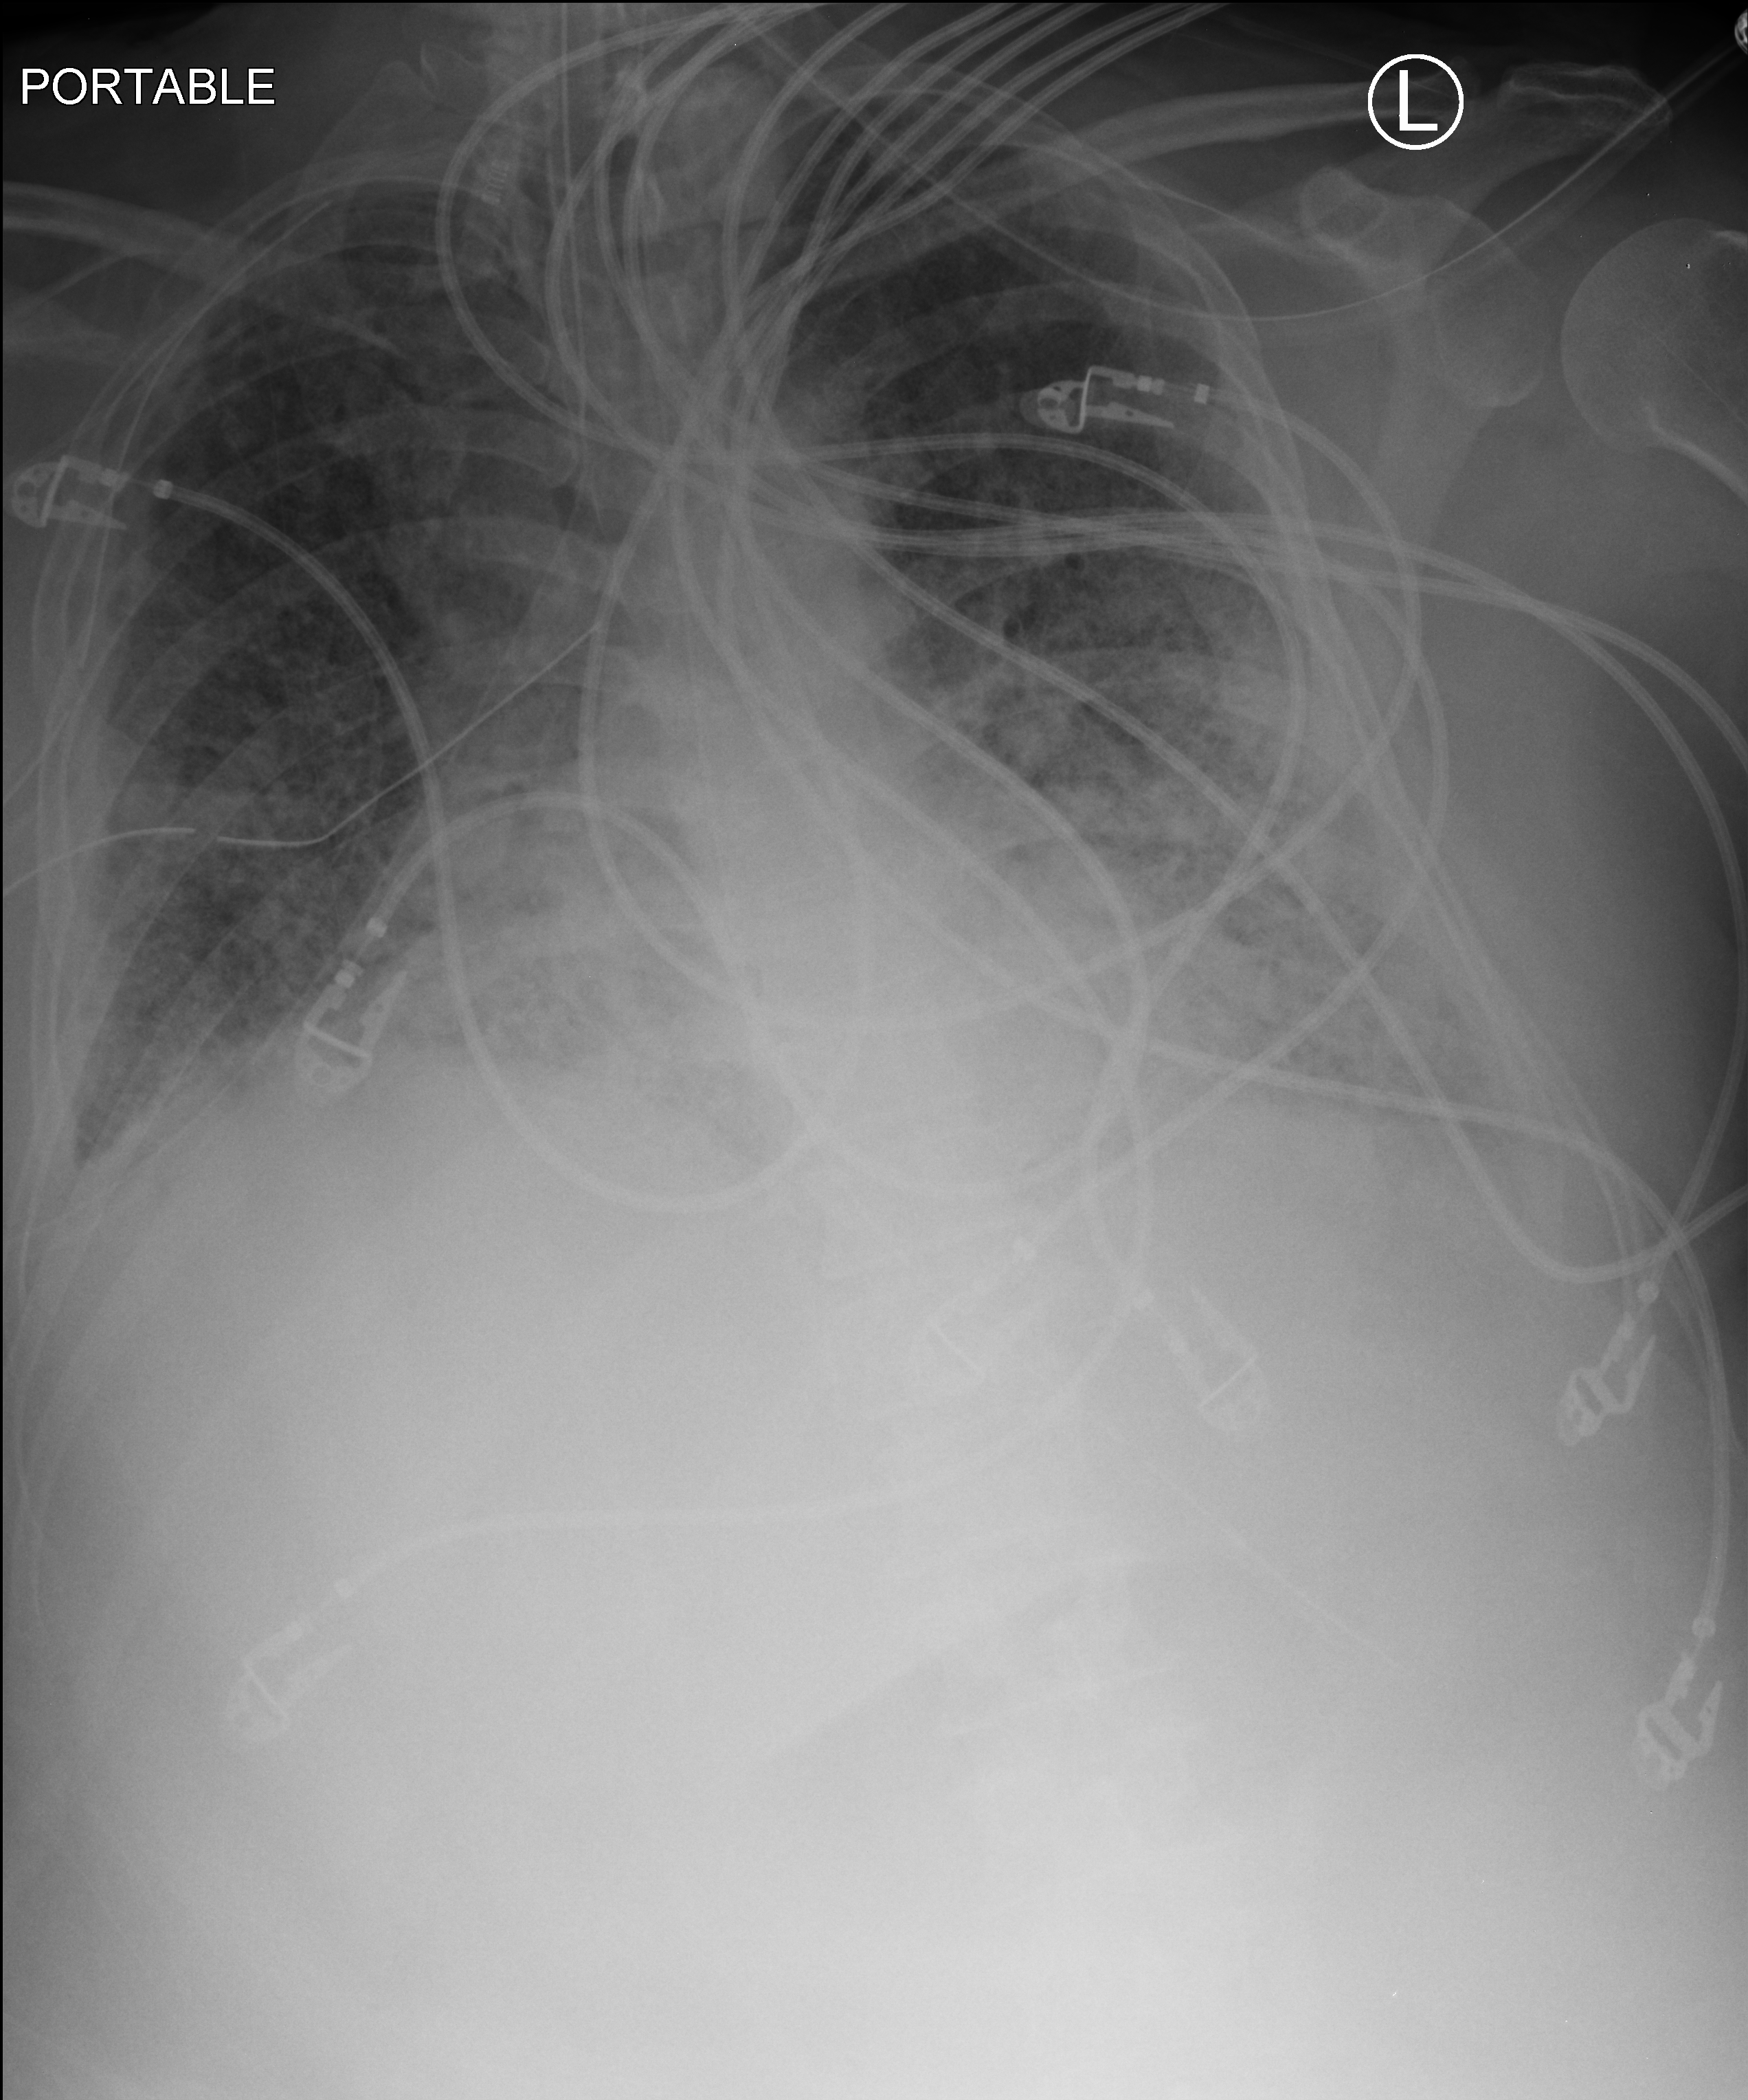
Portable chest radiograph, anteroposterior (AP) projection. Adult patient hospitalised with COVID-19, age 18–59 years.
Admission-level facts for this patient (not findings on this image; timing relative to this image not recorded):
- mechanically ventilated during this hospital stay: yes
- length of hospital stay: 48 days